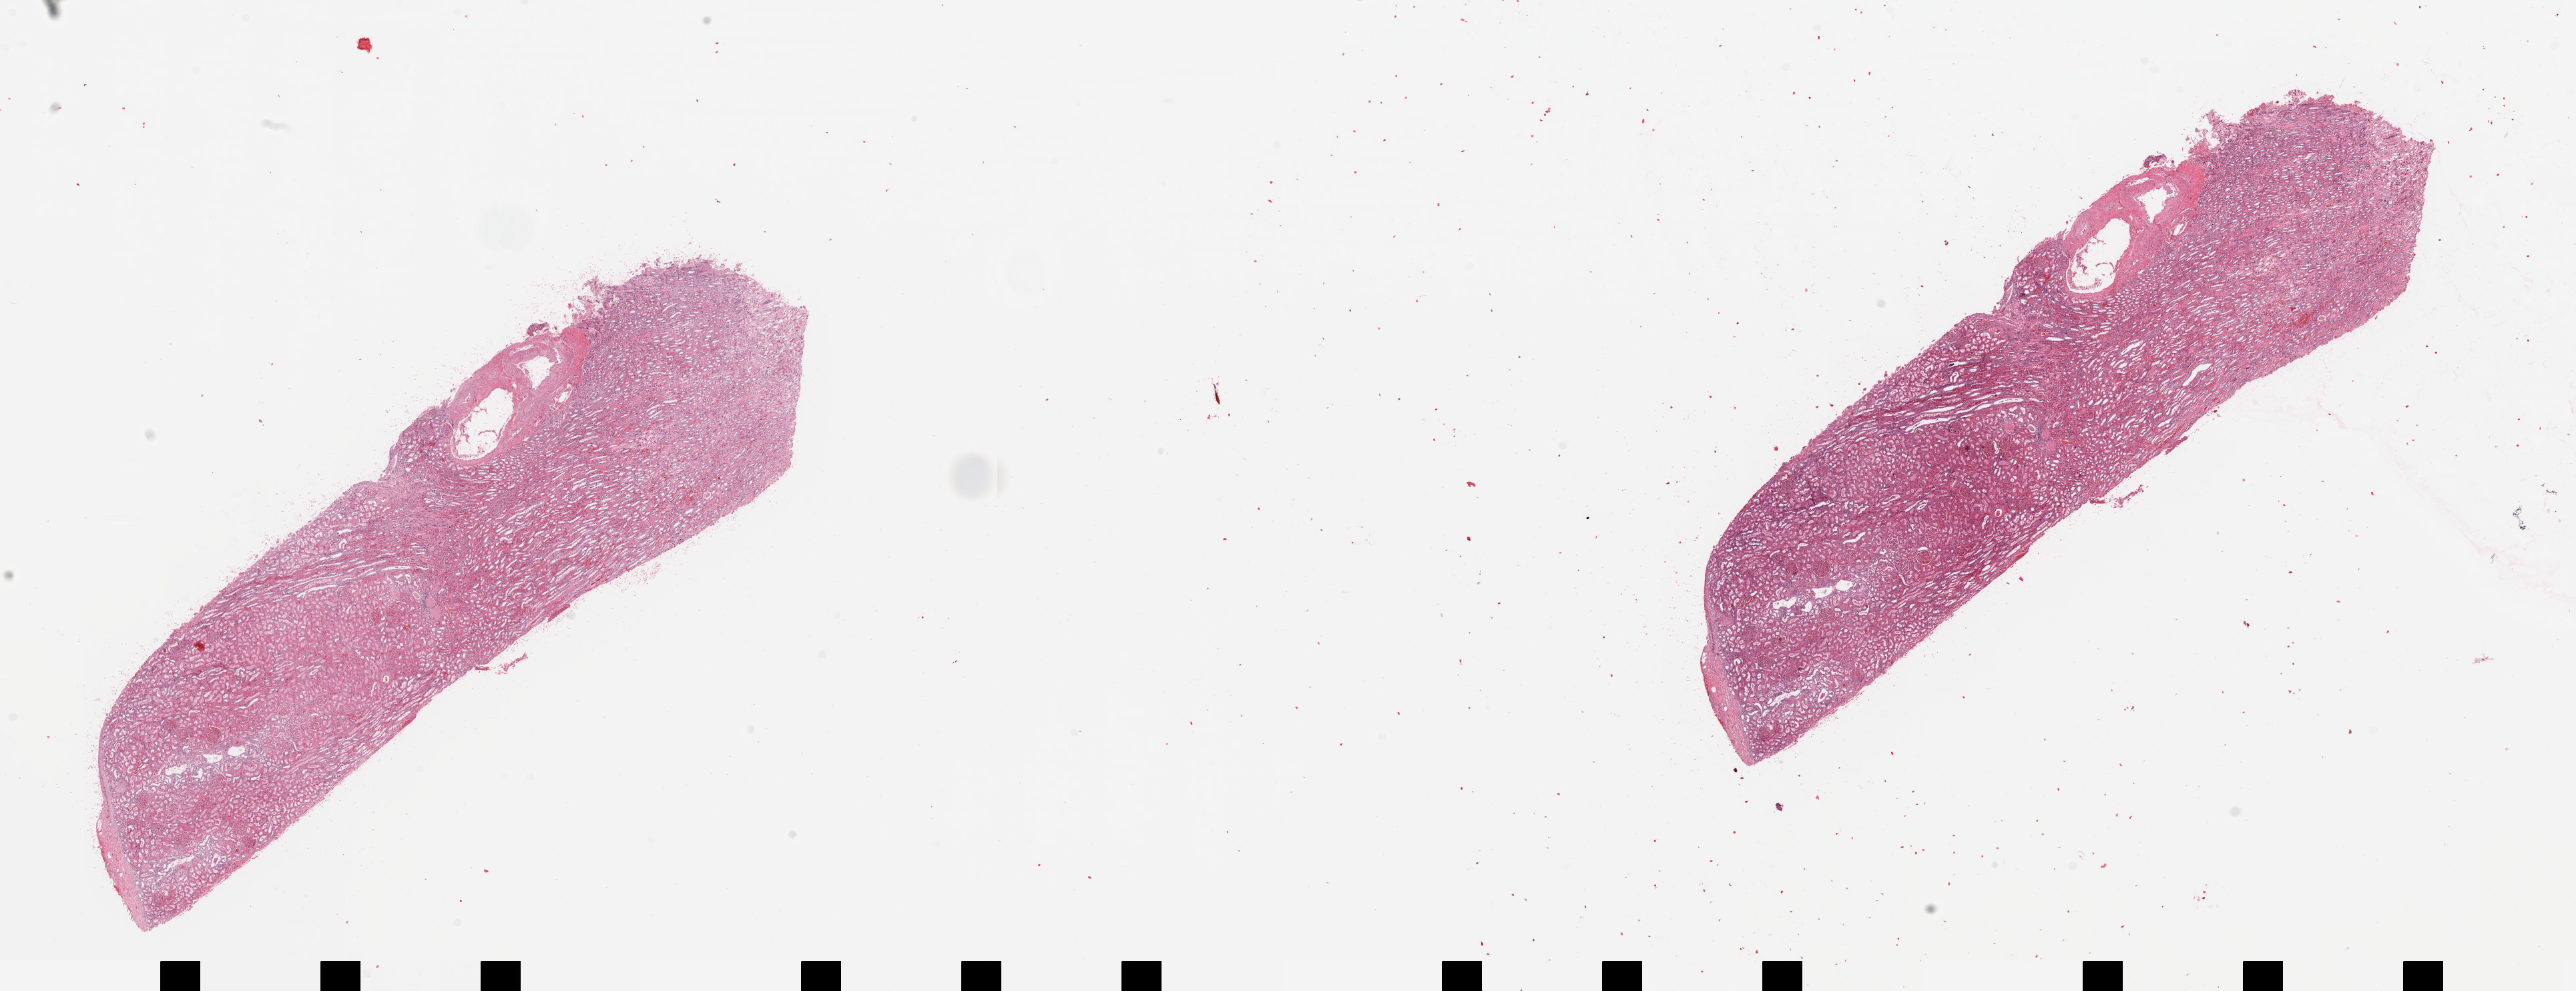
Digitized Hematoxylin and eosin (H&E) stained tissue section (whole slide), shown as a low-resolution overview of the whole scanned area (about 30.5 x 11.7 mm, from a 20x scan). Normal (non-tumour) tissue sample, sampled site: kidney. Patient: male, age 57 years.
- this section: normal (non-tumour) tissue from the same patient
- patient diagnosis: Renal cell carcinoma, NOS